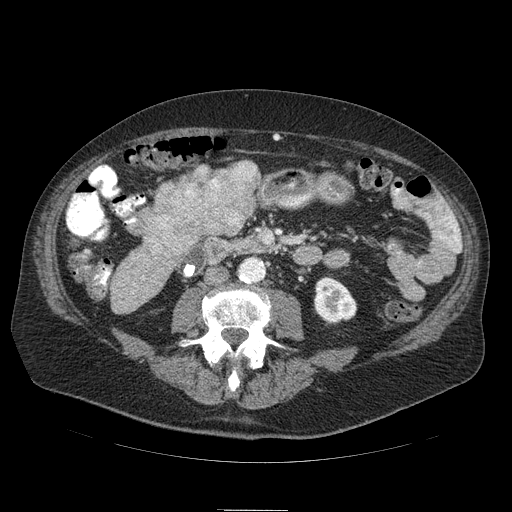
Contrast-enhanced abdominal CT (liver protocol), one axial slice. Slice 15 of 103 in the series (ordered by position). Reconstruction kernel STANDARD. 120 kVp. Soft-tissue window (W 400 / L 40 HU). 2.5 mm slice thickness. 512 × 512 image matrix, field of view 440 × 440 mm. Case-level facts recorded for this patient, not image findings: diagnosis: hepatocellular carcinoma (patient treated with transarterial chemoembolisation; whether this scan precedes or follows treatment is not stated here); TNM stage (as recorded): Stage-IIIA; Child-Pugh class: B.
Annotated regions visible in this slice (semi-automatic segmentation, software-assisted and operator-edited):
- mass: bounding box [x1, y1, x2, y2] px = [134, 159, 264, 262]